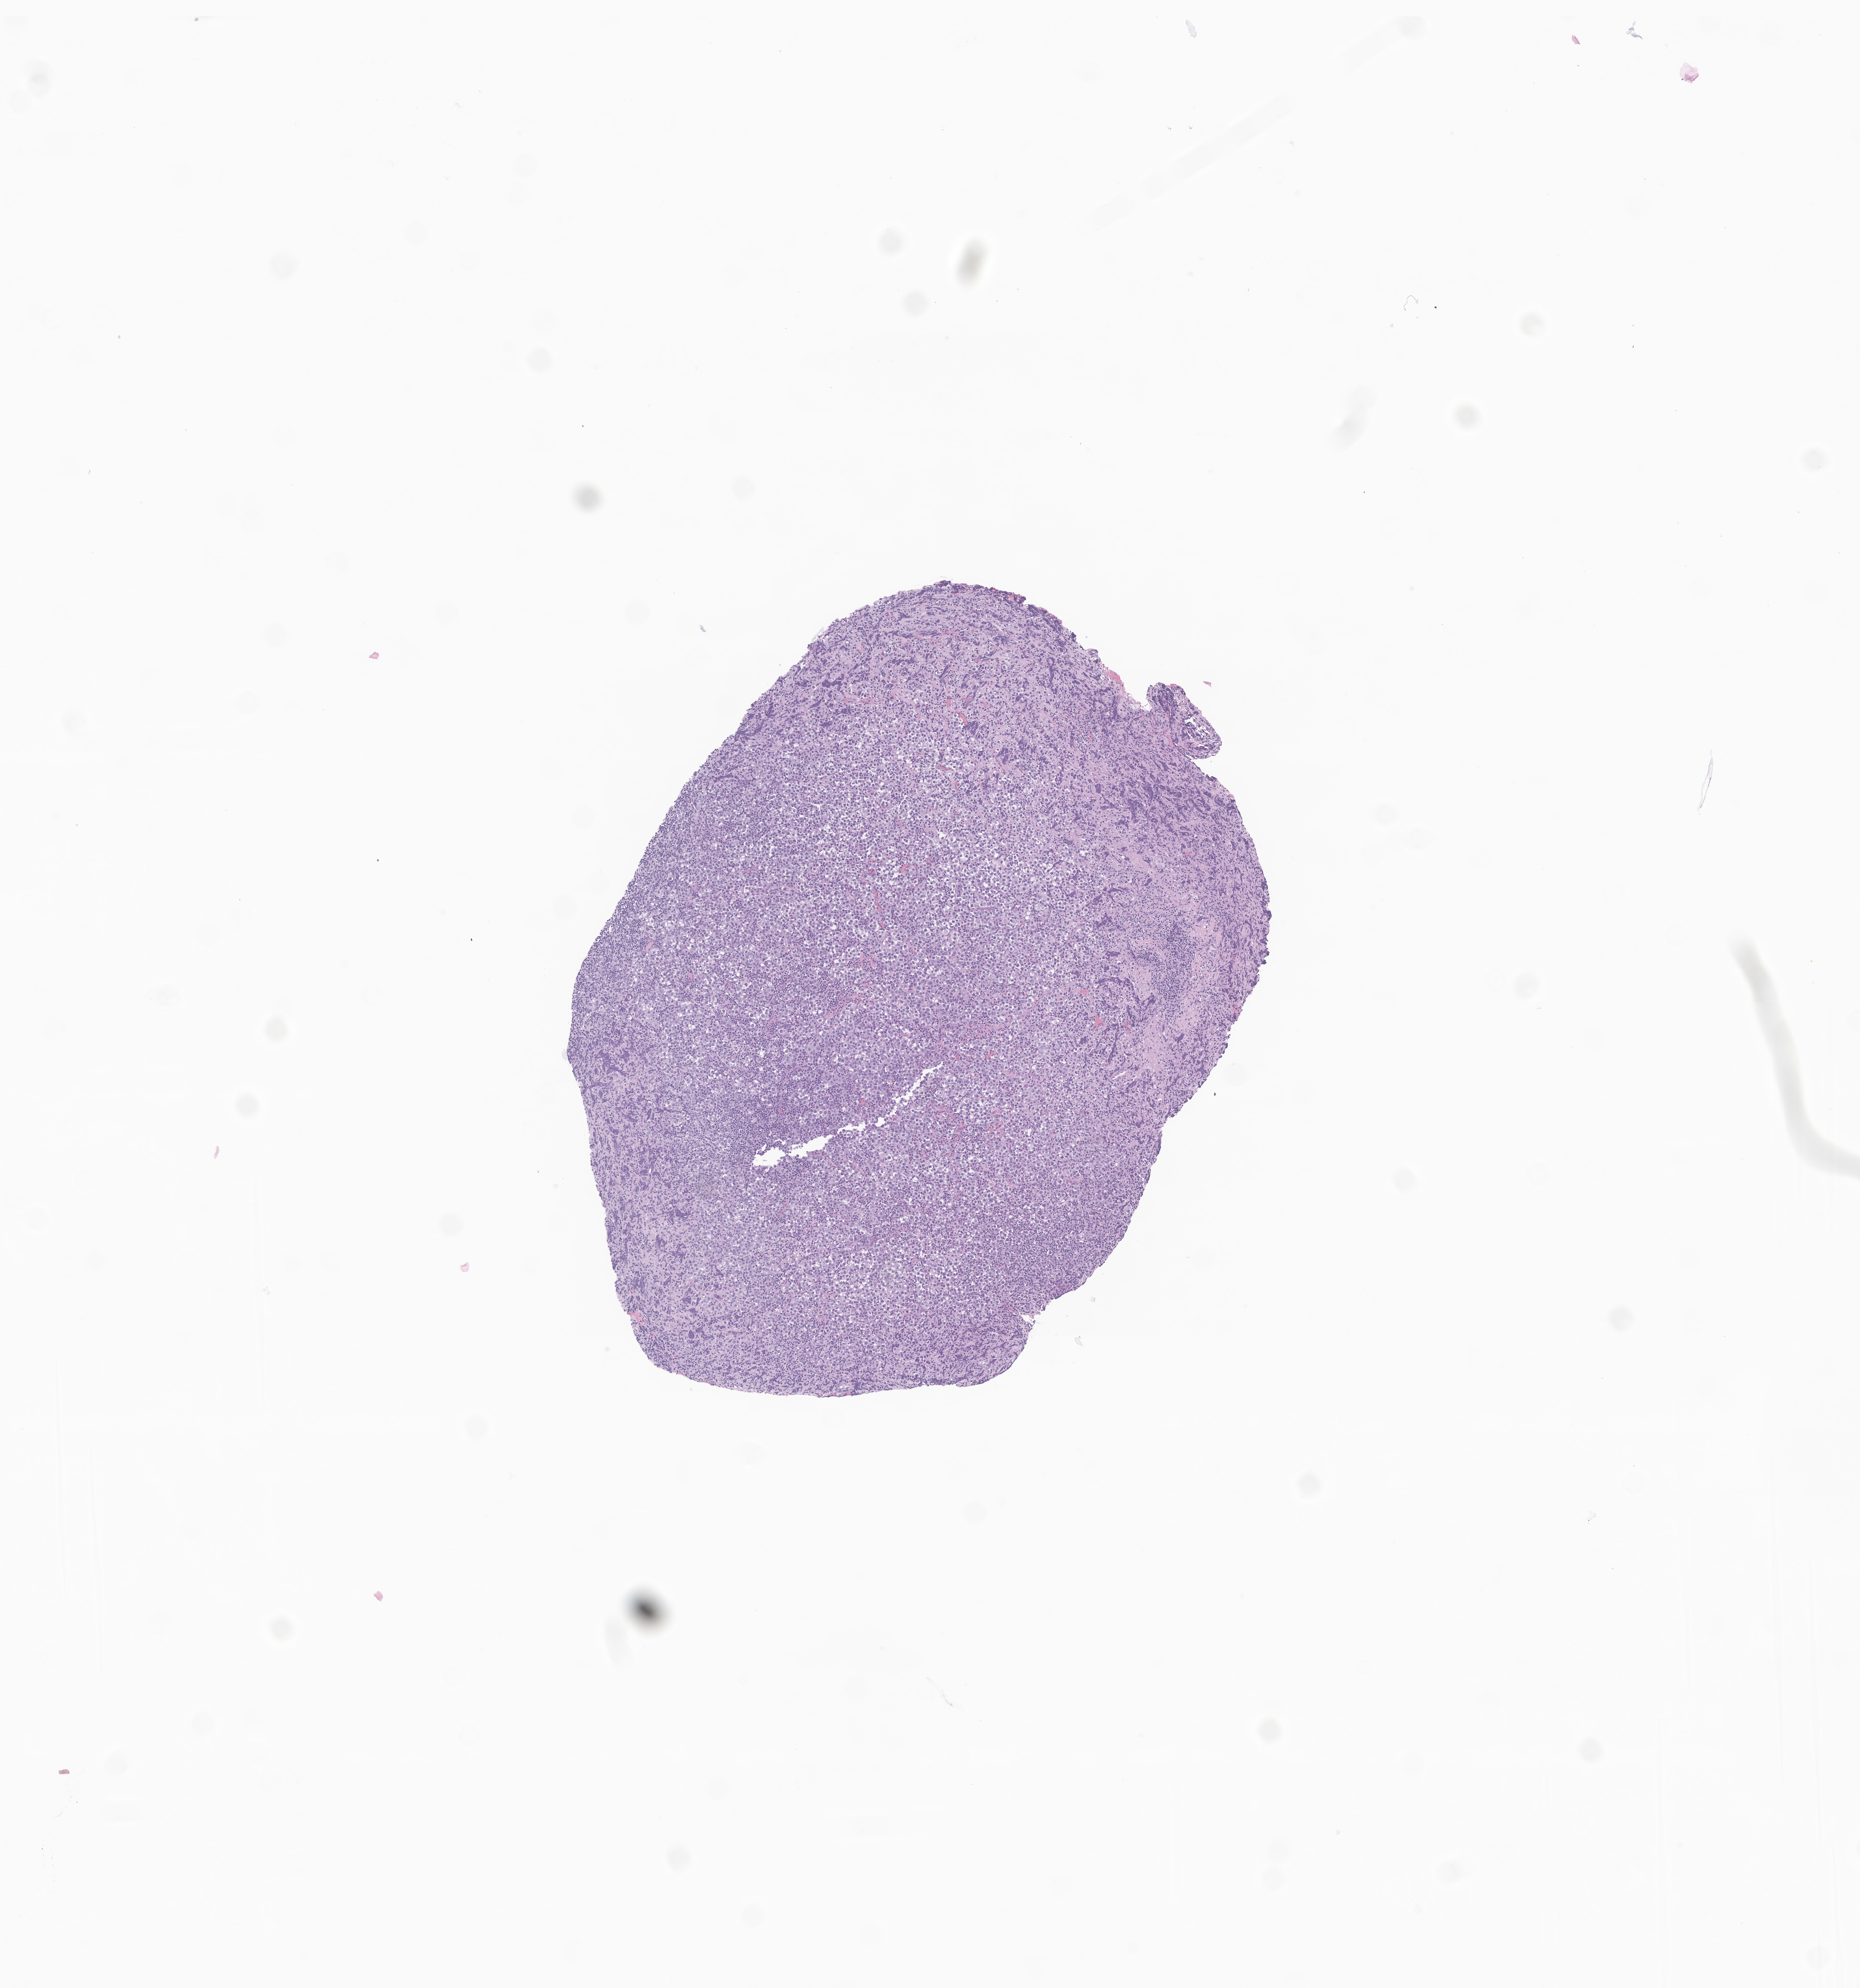
Haematoxylin and eosin whole-slide image of tumor tissue from the brain — whole scanned area (about 5.9 x 6.4 mm) shown as a low-resolution overview; FFPE section. Patient: female, age 102 months (8 years 6 months).
Recorded diagnosis: Germinoma.